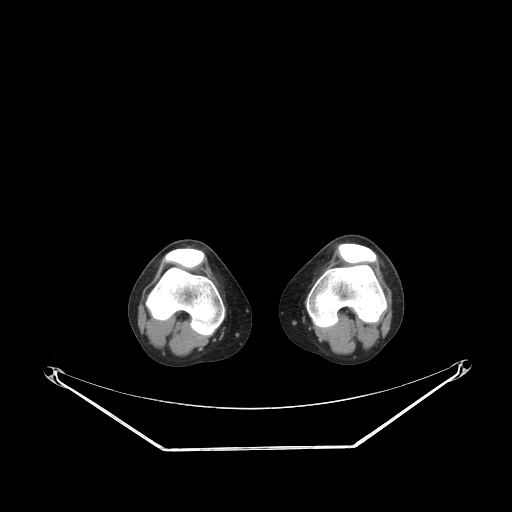
CT of an extremity soft-tissue mass (from a PET/CT study), one axial slice. Slice 163 of 223 in the series (ordered by position). Reconstruction kernel STANDARD. 140 kVp. Soft-tissue window (W 400 / L 40 HU). 512 × 512 image matrix. Female patient. Case-level facts recorded for this patient, not image findings: histological type: spindle cell suggestive of biphasic synovial sarcoma; grade: intermediate; site of the primary tumour: left knee.
Structures marked on this image (expert contour drawn on MRI and transferred to this co-registered scan by the dataset authors):
- gross tumour volume including surrounding oedema: bounding box <381,285,387,293> (left, top, right, bottom; pixels)